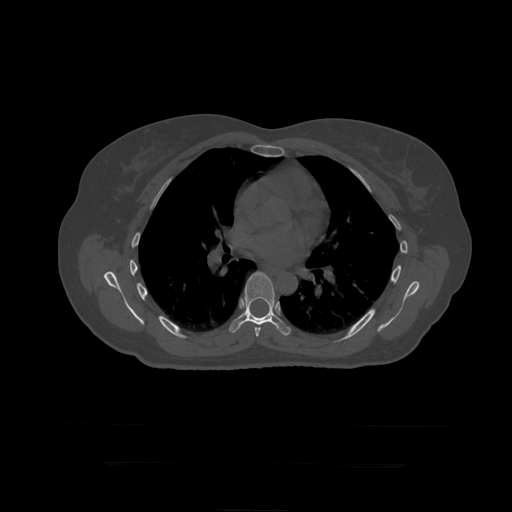
CT including the spine, one axial slice. Bone window (W 1800 / L 400 HU). 512 × 512 image matrix. Patient age 41 years. Case-level facts recorded for this patient, not image findings: primary cancer: breast.
Outlined on this slice (semi-automatically segmented with operator editing):
- T7 vertebra: bounding box [x1, y1, x2, y2] px = [255, 327, 261, 337]
- T8 vertebra: [229, 272, 291, 336]